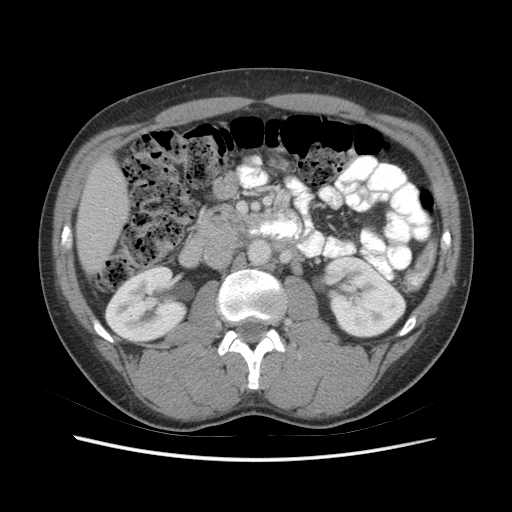
Contrast-enhanced abdominal CT (liver protocol), one axial slice. Position 15 of 73 along the scan axis. 140 kVp. Soft-tissue window (W 400 / L 40 HU). 2.5 mm slice thickness. 512 × 512 image matrix, field of view 360 × 360 mm. From the clinical record (not read from this slice): diagnosis: hepatocellular carcinoma (patient treated with transarterial chemoembolisation; whether this scan precedes or follows treatment is not stated here); TNM stage (as recorded): Stage-IIIA; Child-Pugh class: A.
Structures marked on this image (semi-automatically segmented with operator editing):
- liver parenchyma outside the tumour (the mass and vessels are separate outlines, so this box may not span the whole liver): bounding box <76,156,128,274> (left, top, right, bottom; pixels)